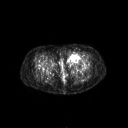
FDG PET of an extremity soft-tissue mass (from a PET/CT study), one axial slice; position 40 of 267 along the scan axis; 3.27 mm slice thickness; 128 × 128 image matrix, field of view 700 × 700 mm. Patient: female, 47 years. Case-level facts recorded for this patient, not image findings: histological type: myxofibrosarcoma; grade: intermediate; site of the primary tumour: left thigh.
Outlined on this slice (expert contour drawn on MRI and transferred to this co-registered scan by the dataset authors):
- gross tumour volume including surrounding oedema: box from (x=65, y=53) to (x=83, y=64) px
- gross tumour volume (mass): (x=67, y=53)–(x=80, y=62)